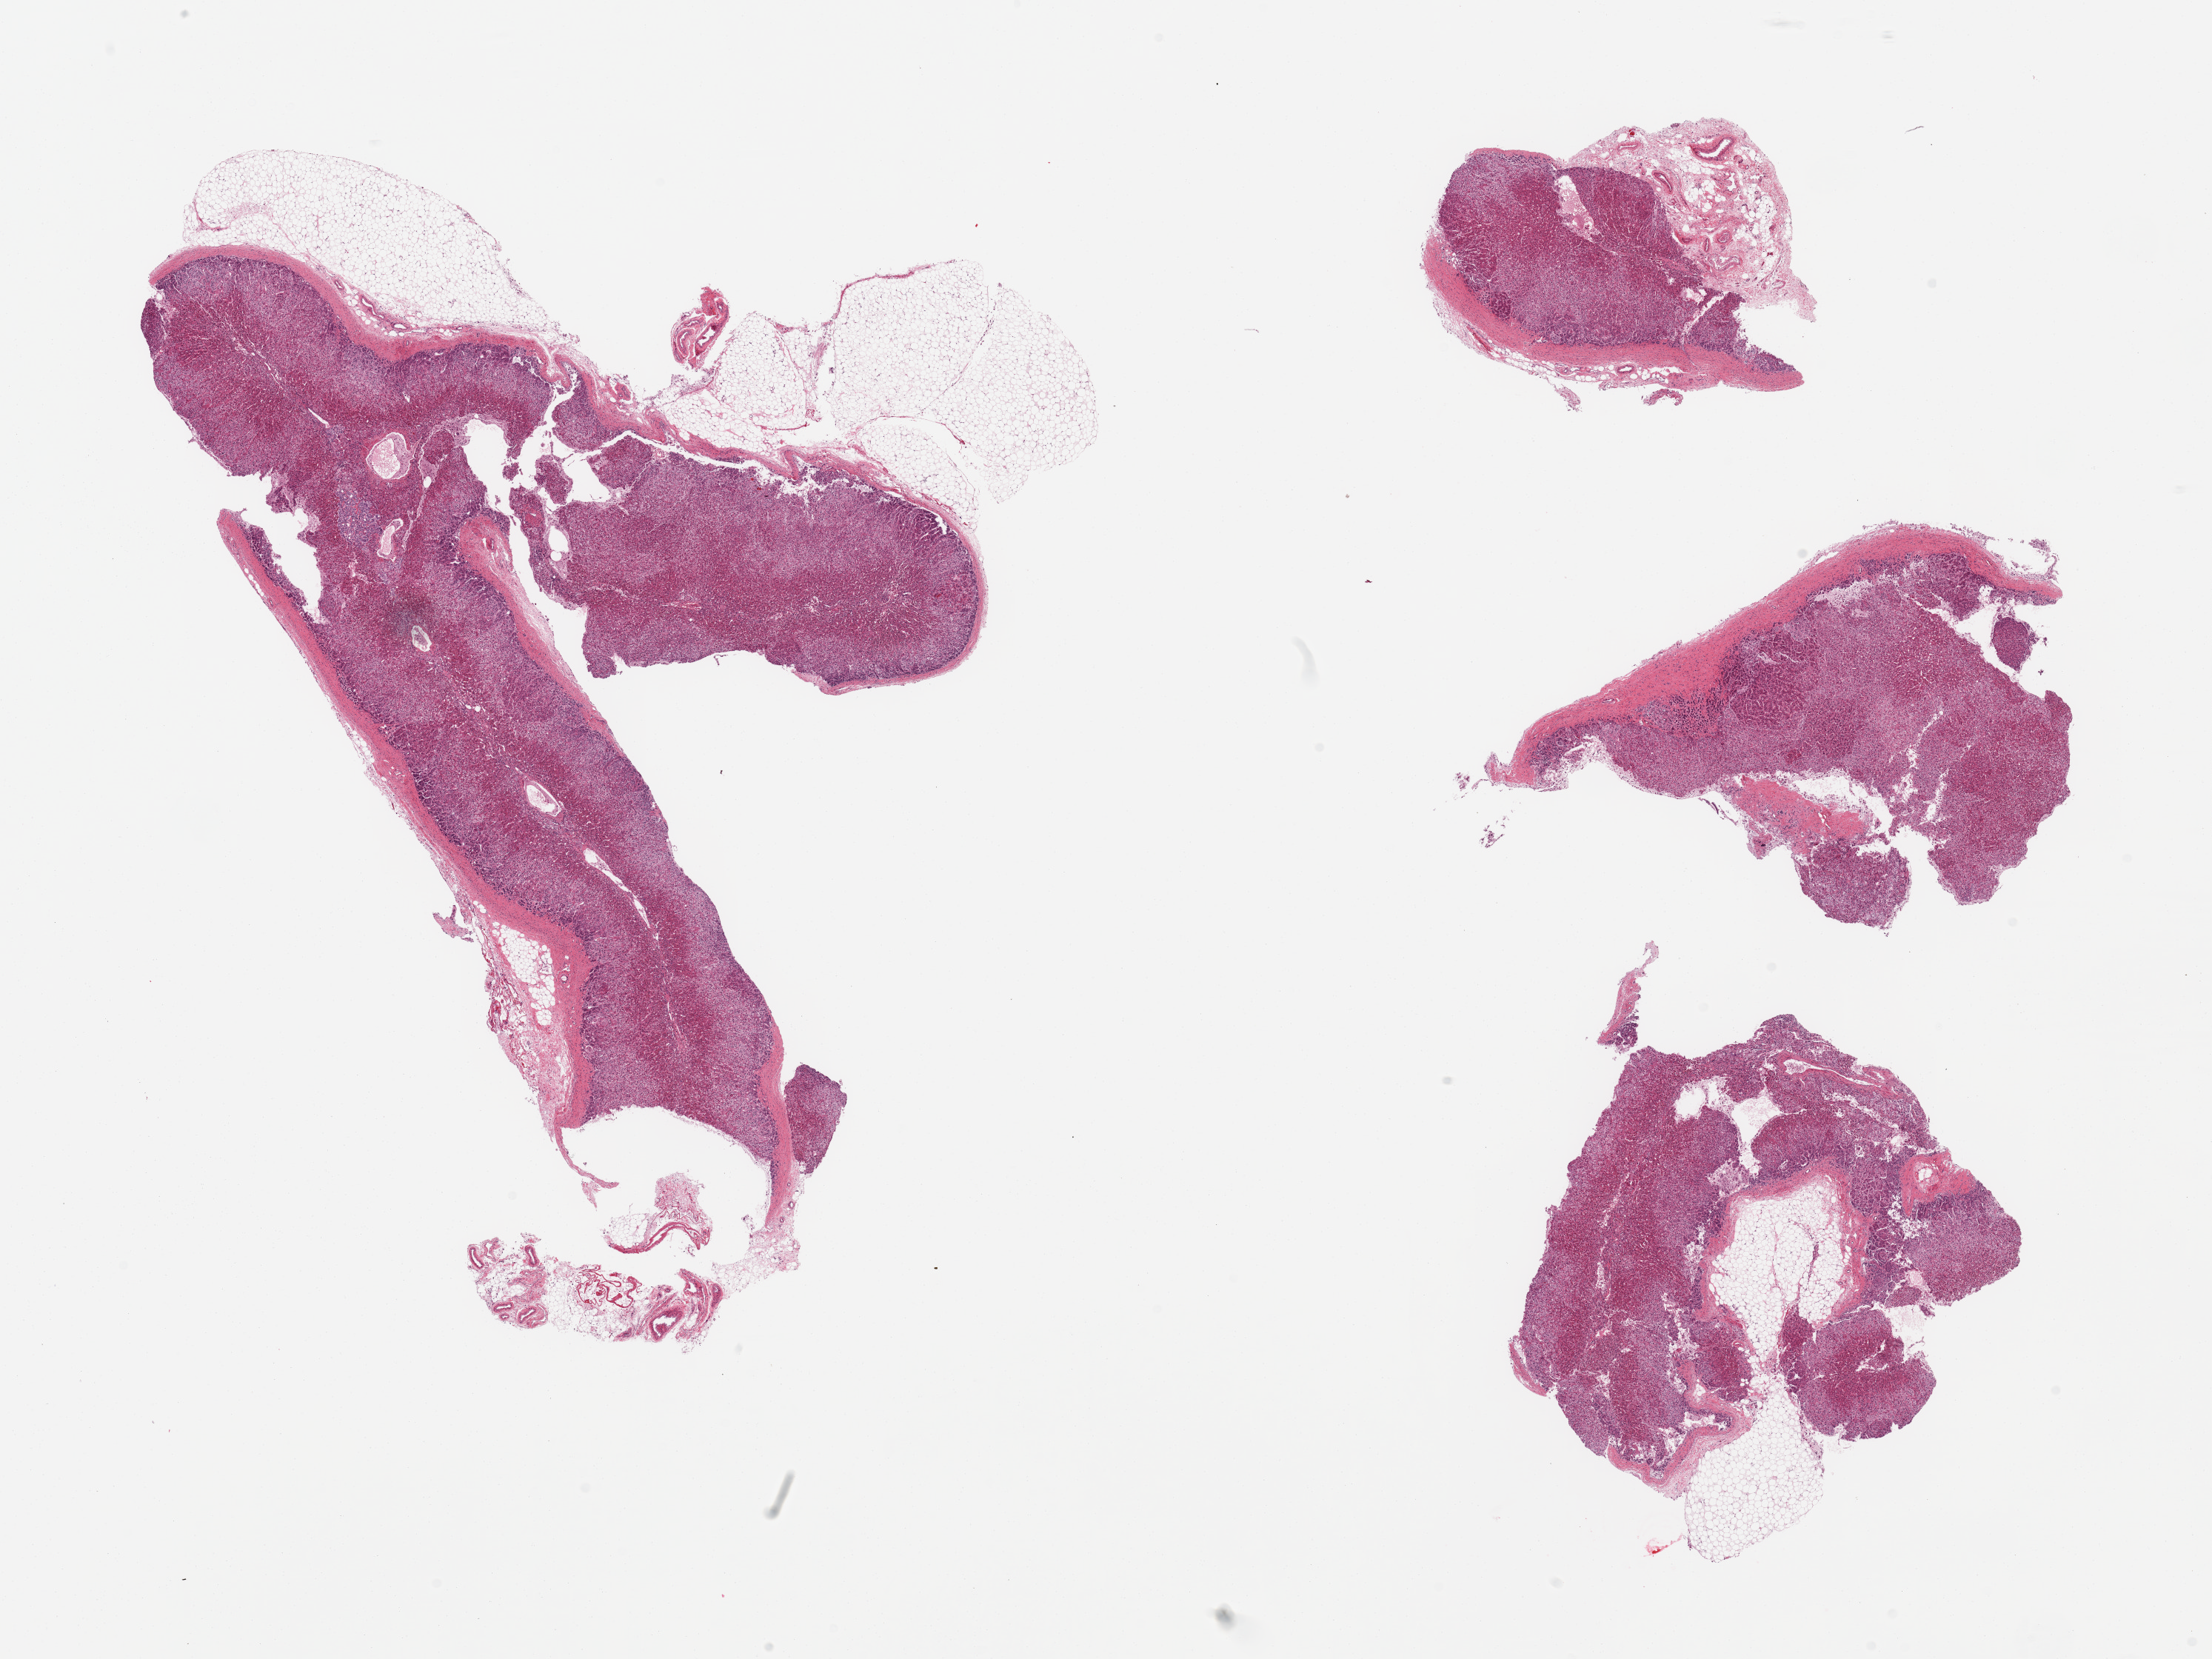
Digitized H&E-stained section, whole scanned area (about 23.6 x 17.7 mm, acquisition: 20x scan) shown as a low-resolution overview, PAXgene-fixed paraffin-embedded (PFPE) section, sampled site (target tissue): adrenal gland, donor tissue sample. Female donor.
- reviewer comment on this tissue sample: 4 pieces, cortex, ~10-20% adherent fat